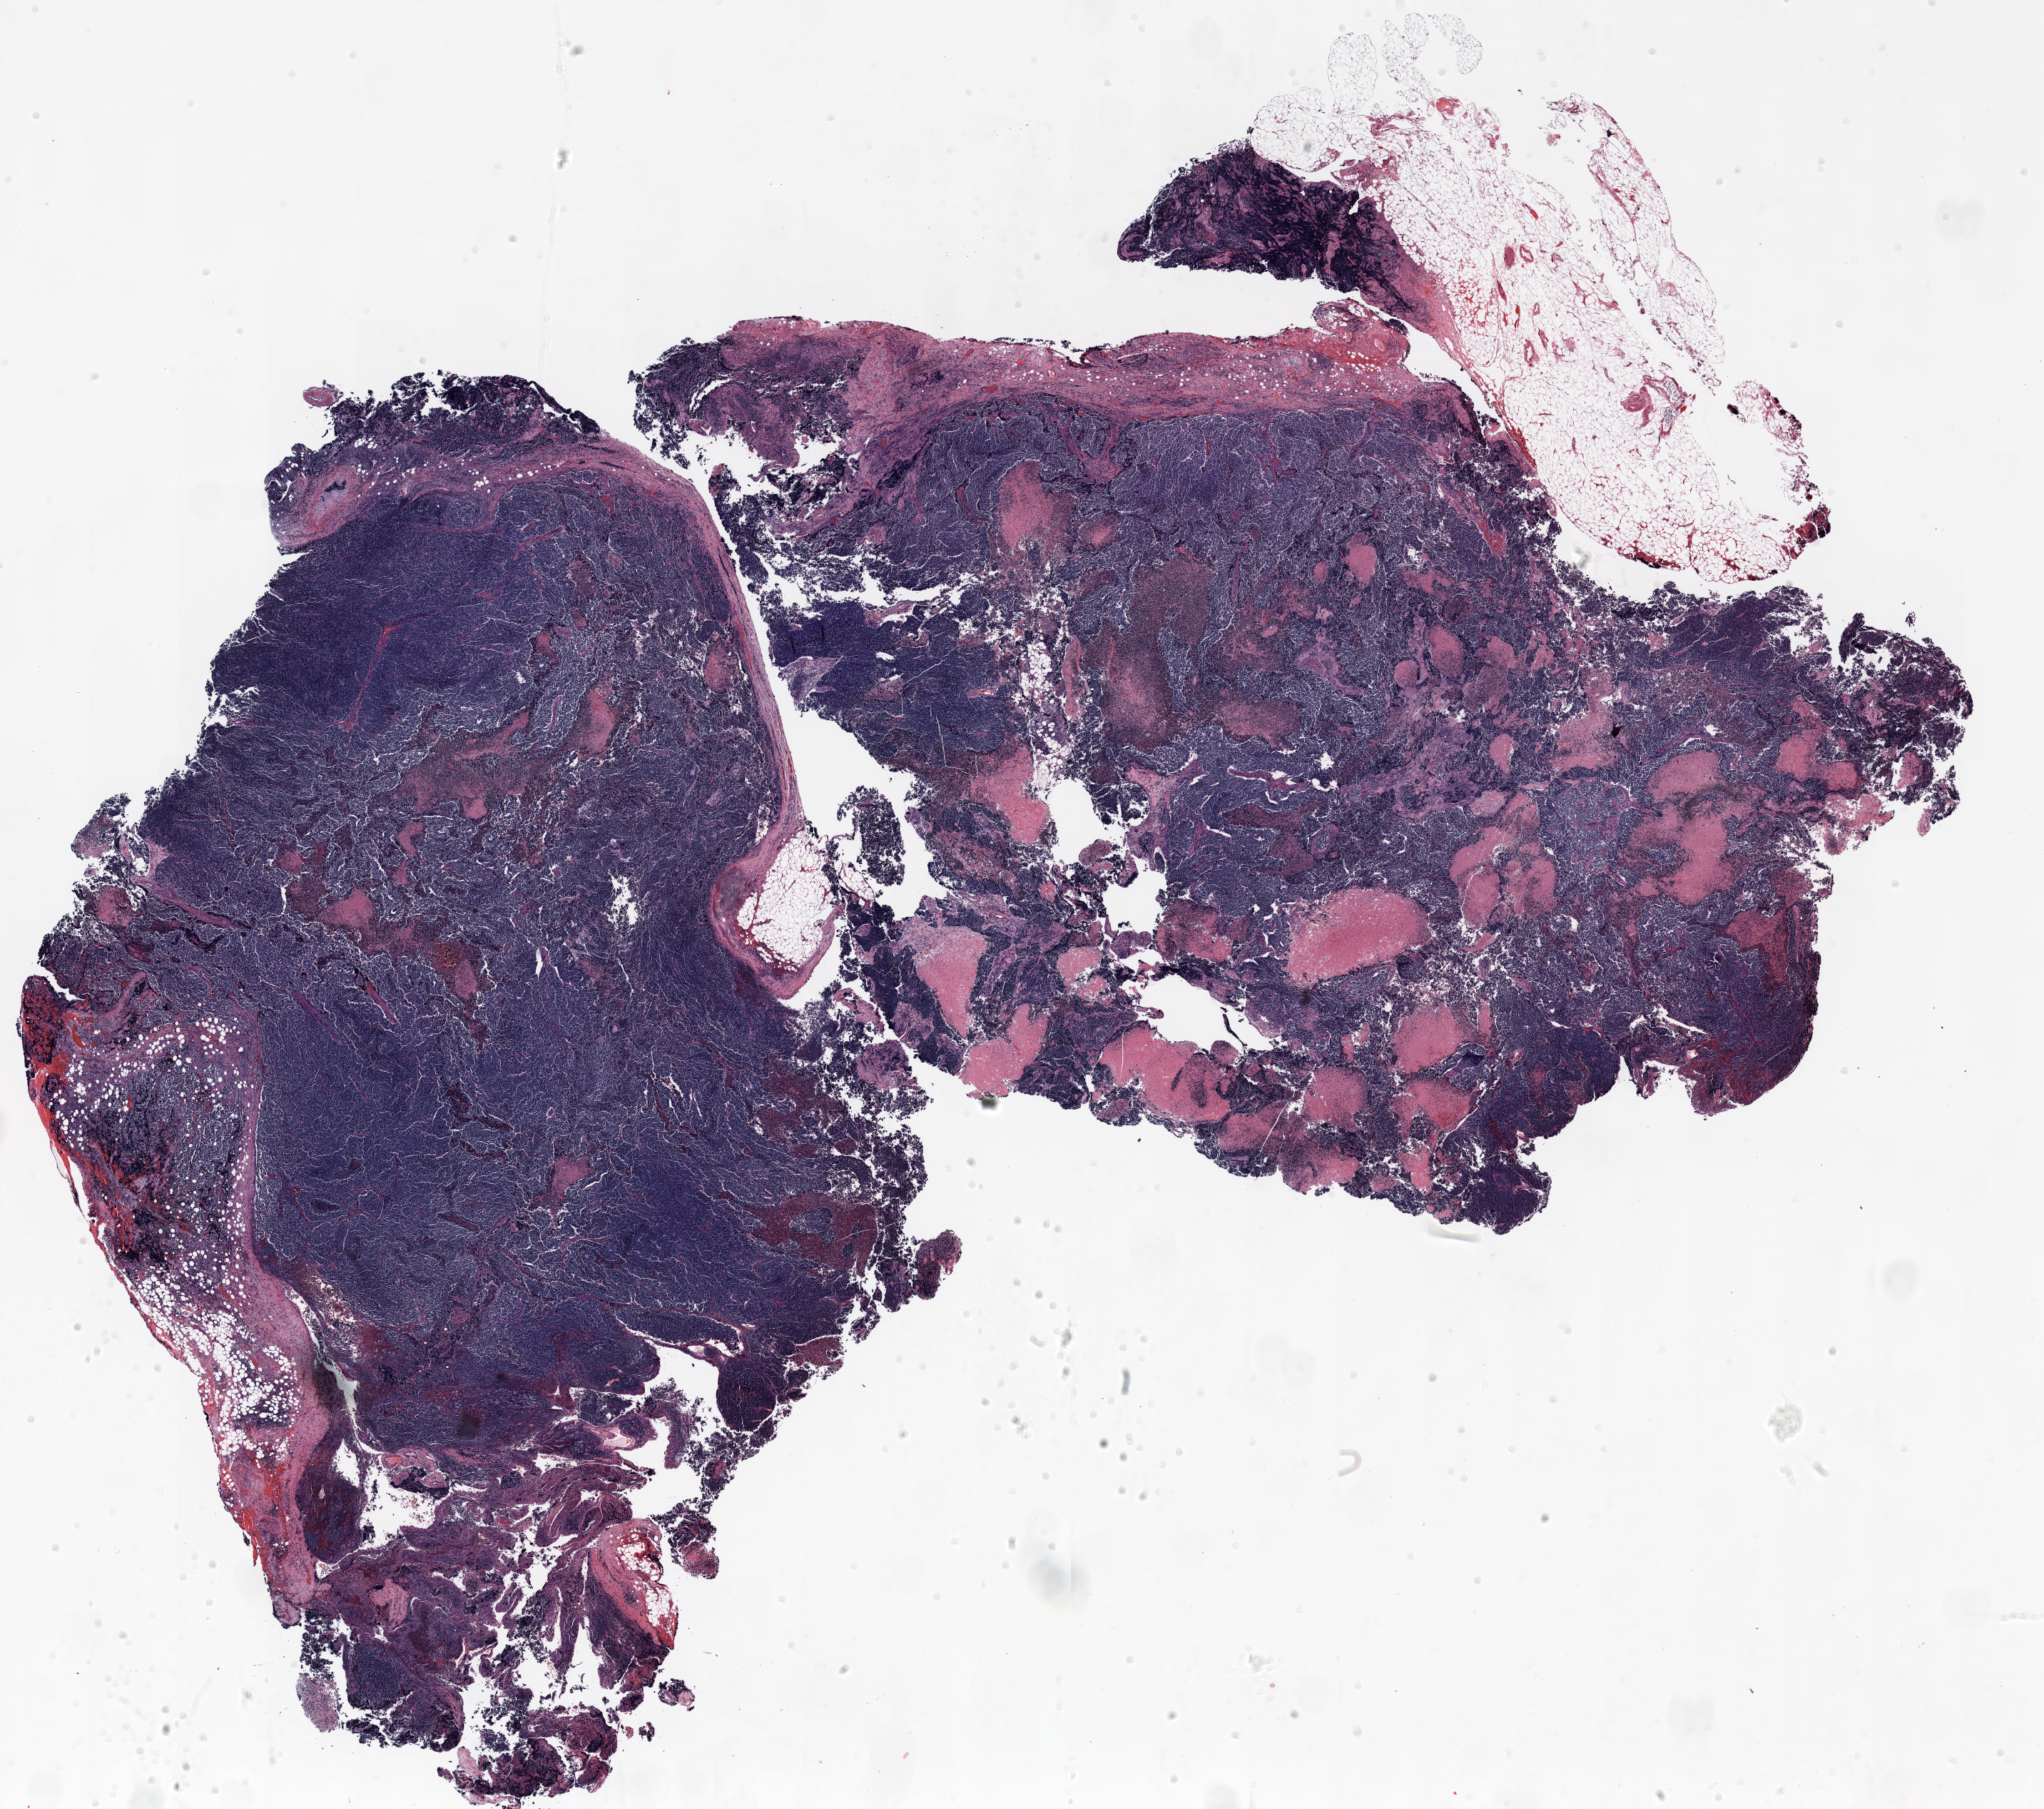
Whole-slide histology image, H&E — a low-resolution overview of the entire scanned area, about 23.0 x 20.4 mm, formalin-fixed paraffin-embedded (FFPE) section, lung. Female, age 72 at enrolment. Former smoker at enrolment. Grade: cannot be assessed (GX).
* stage (AJCC 6th edition): IV
* primary tumour location (clinical record): mediastinum
* ICD-O-3 topography: lung, NOS (C34.9)
* tumour size (pathology): 70 mm
* participant's lung-cancer diagnosis: Small cell carcinoma, NOS